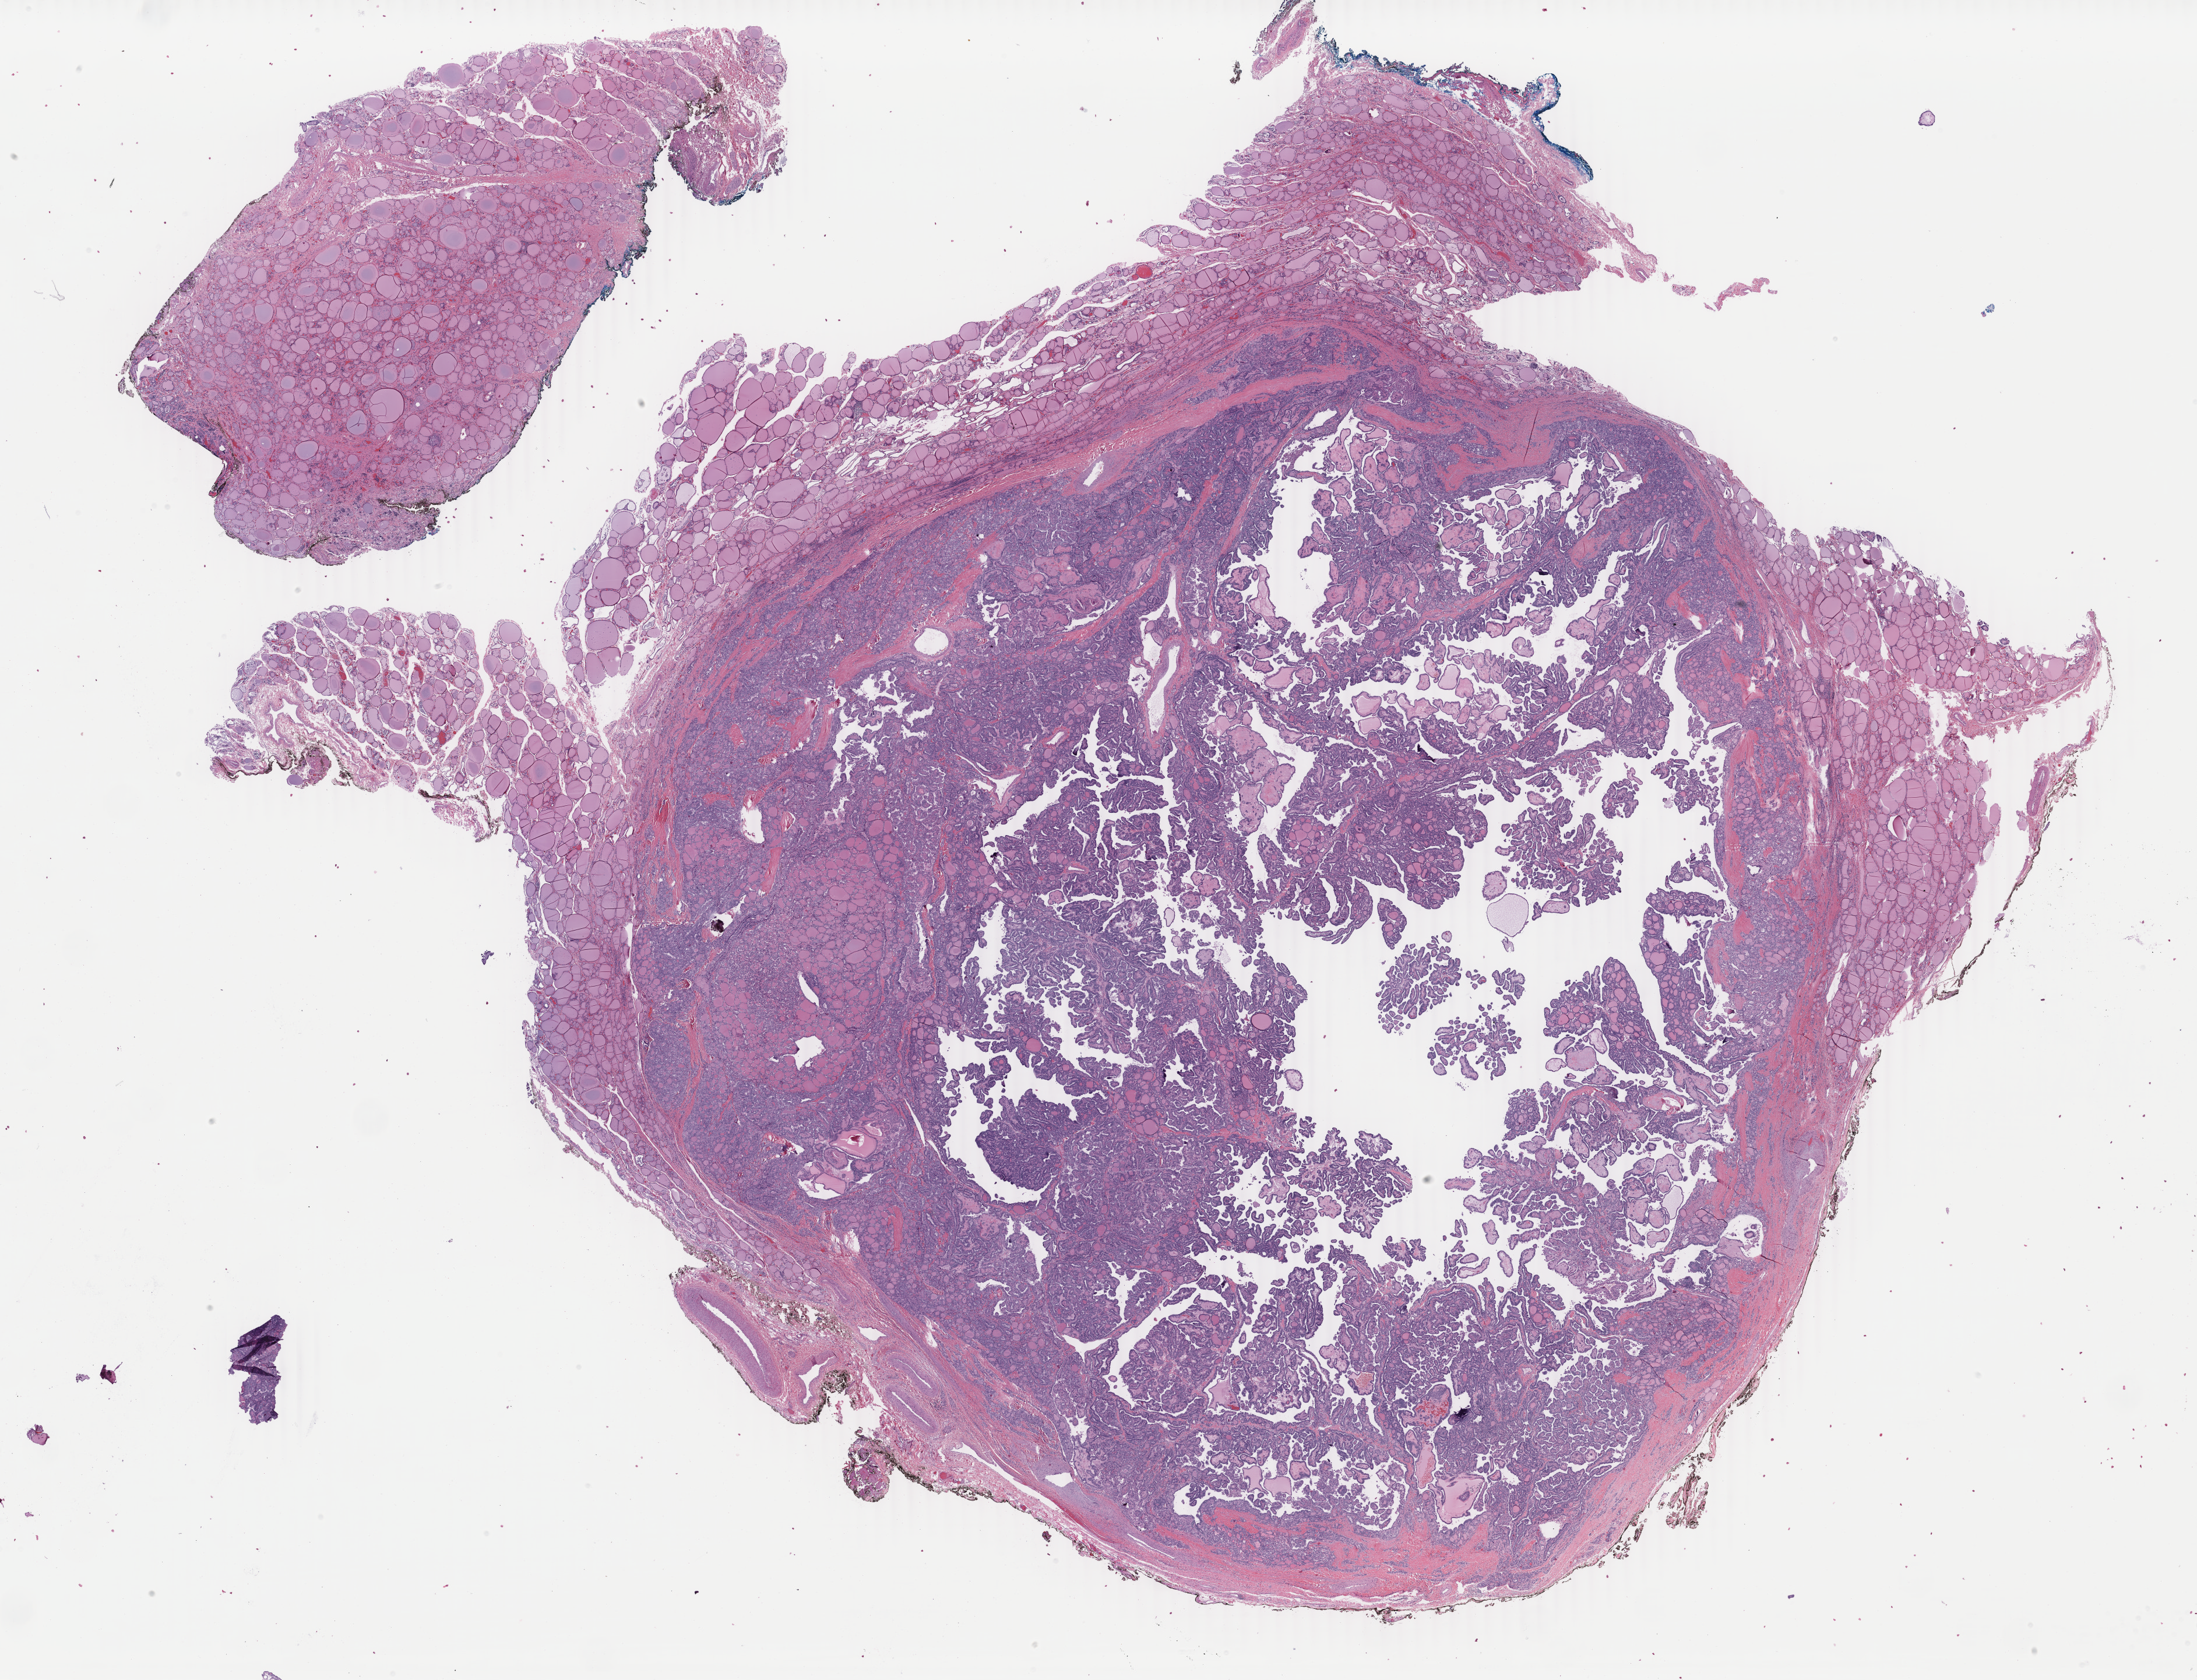
Whole-slide histology image, Hematoxylin and eosin (H&E) stained — shown as a low-resolution overview of the whole scanned area (about 30.0 x 22.9 mm, from a 40x scan); formalin-fixed paraffin-embedded (FFPE) diagnostic section; primary tumour sample from the thyroid. Female, age 41 years at initial diagnosis.
AJCC pathologic stage: I (7th edition). TNM: T2 N0 M0. Lymph nodes positive (case pathology): 0 of 1 examined. Histologic diagnosis: Papillary adenocarcinoma, NOS (thyroid gland).